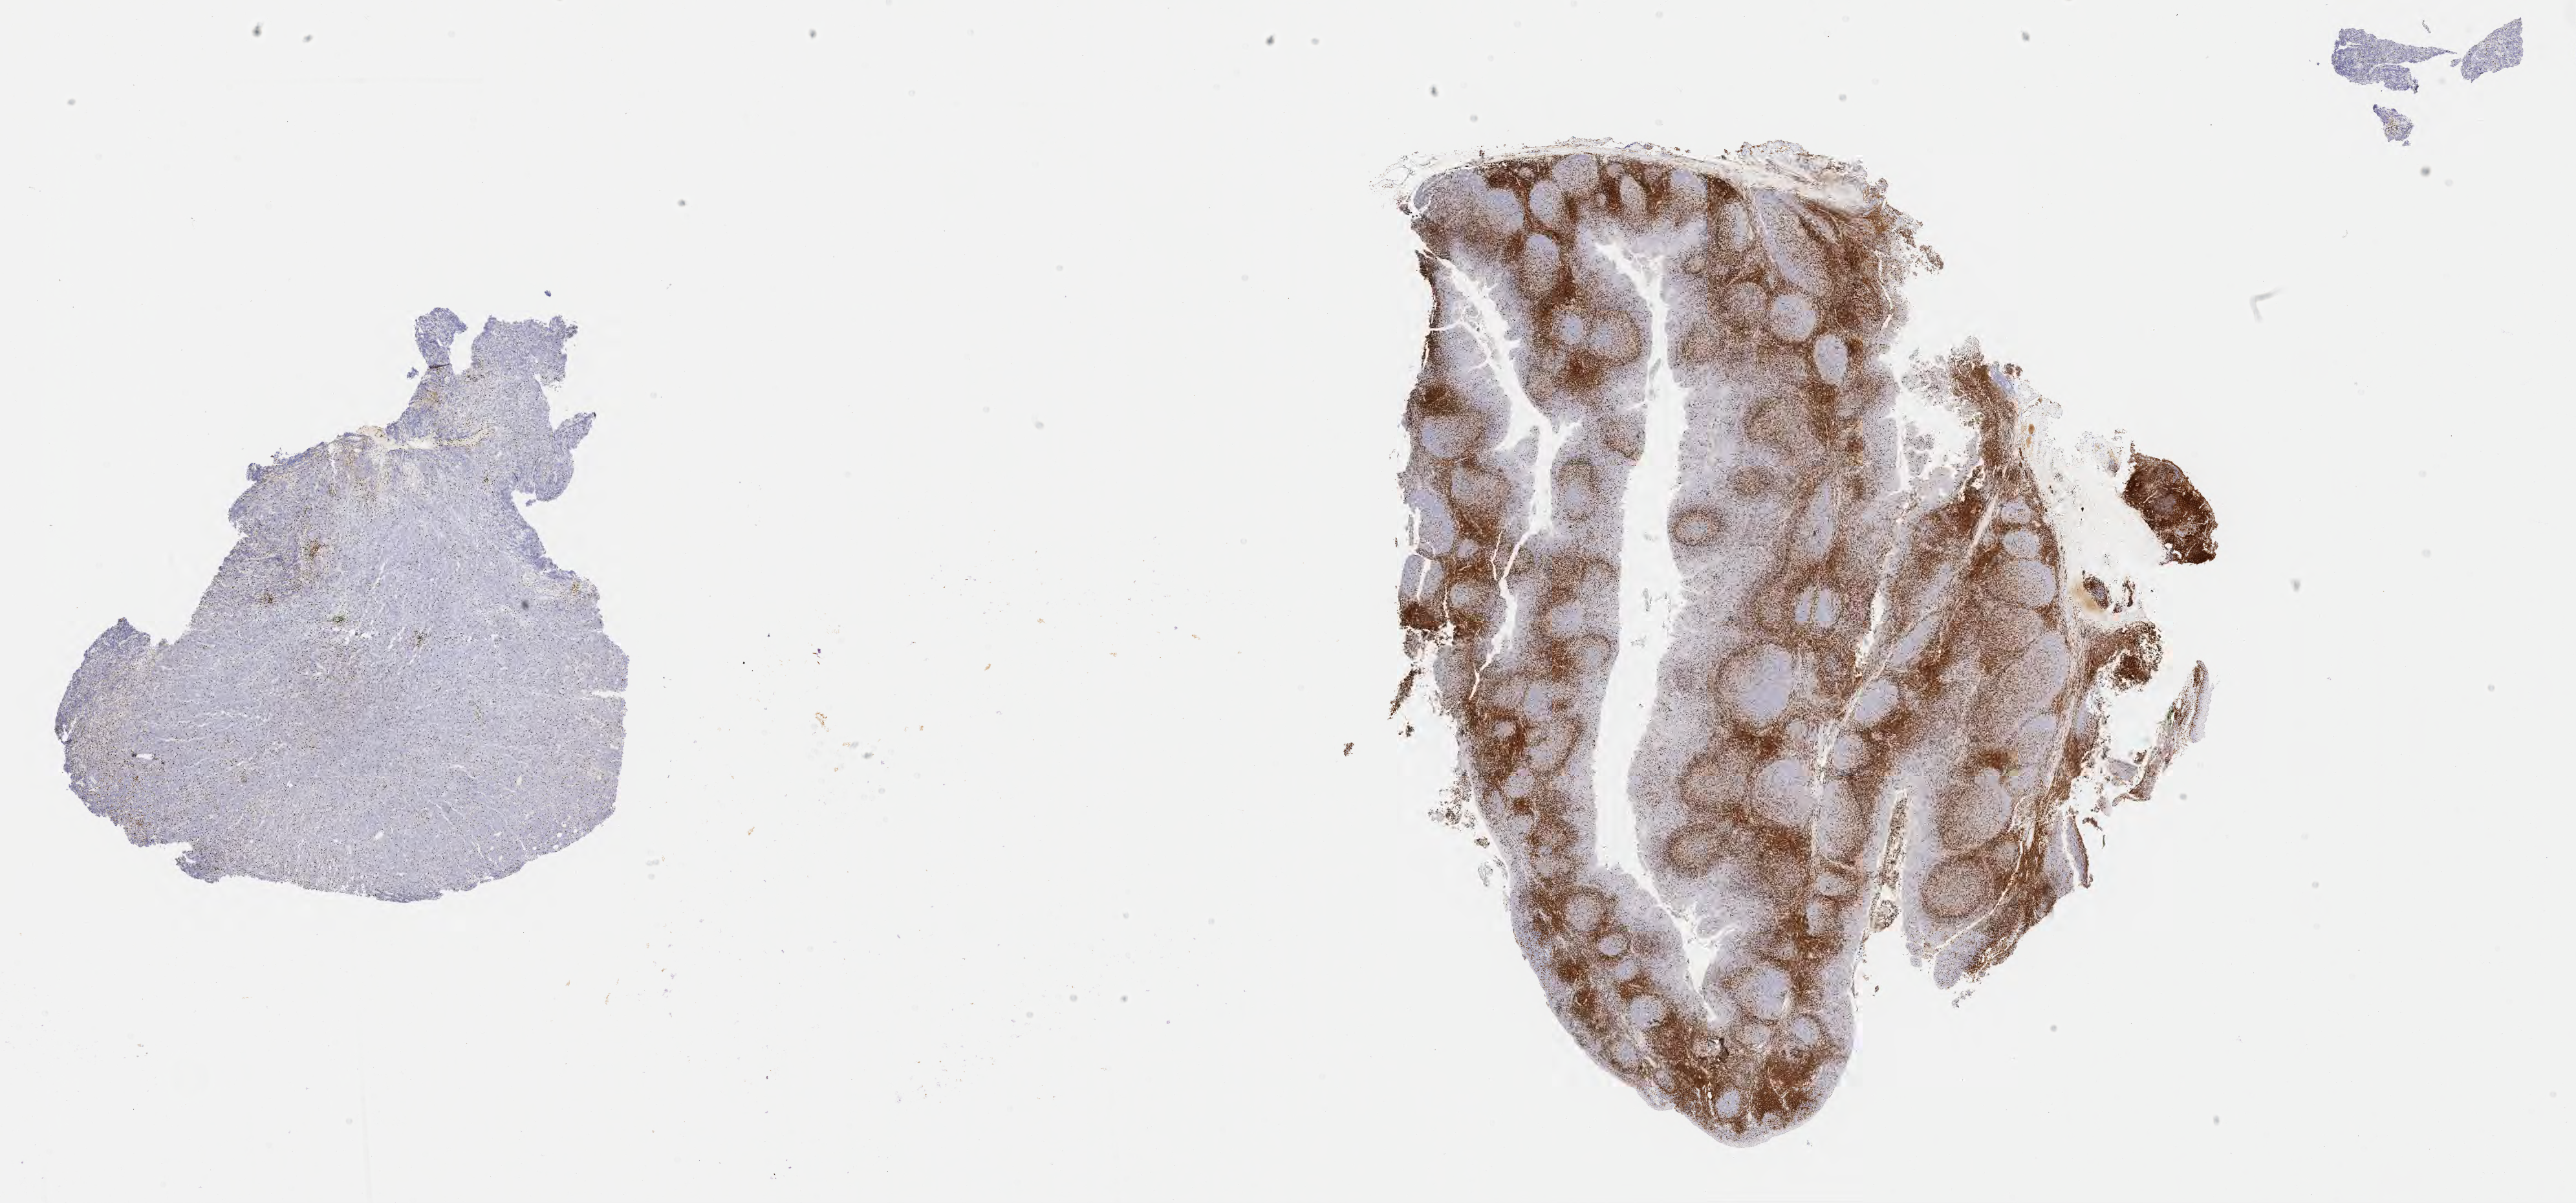
IHC for CD3, whole-slide image — whole scanned area (about 32.2 x 15.0 mm) shown as a low-resolution overview, specimen: tumor tissue, site: mandible. Female patient; age at initial diagnosis 5 years.
- diagnosis: Burkitt lymphoma, NOS